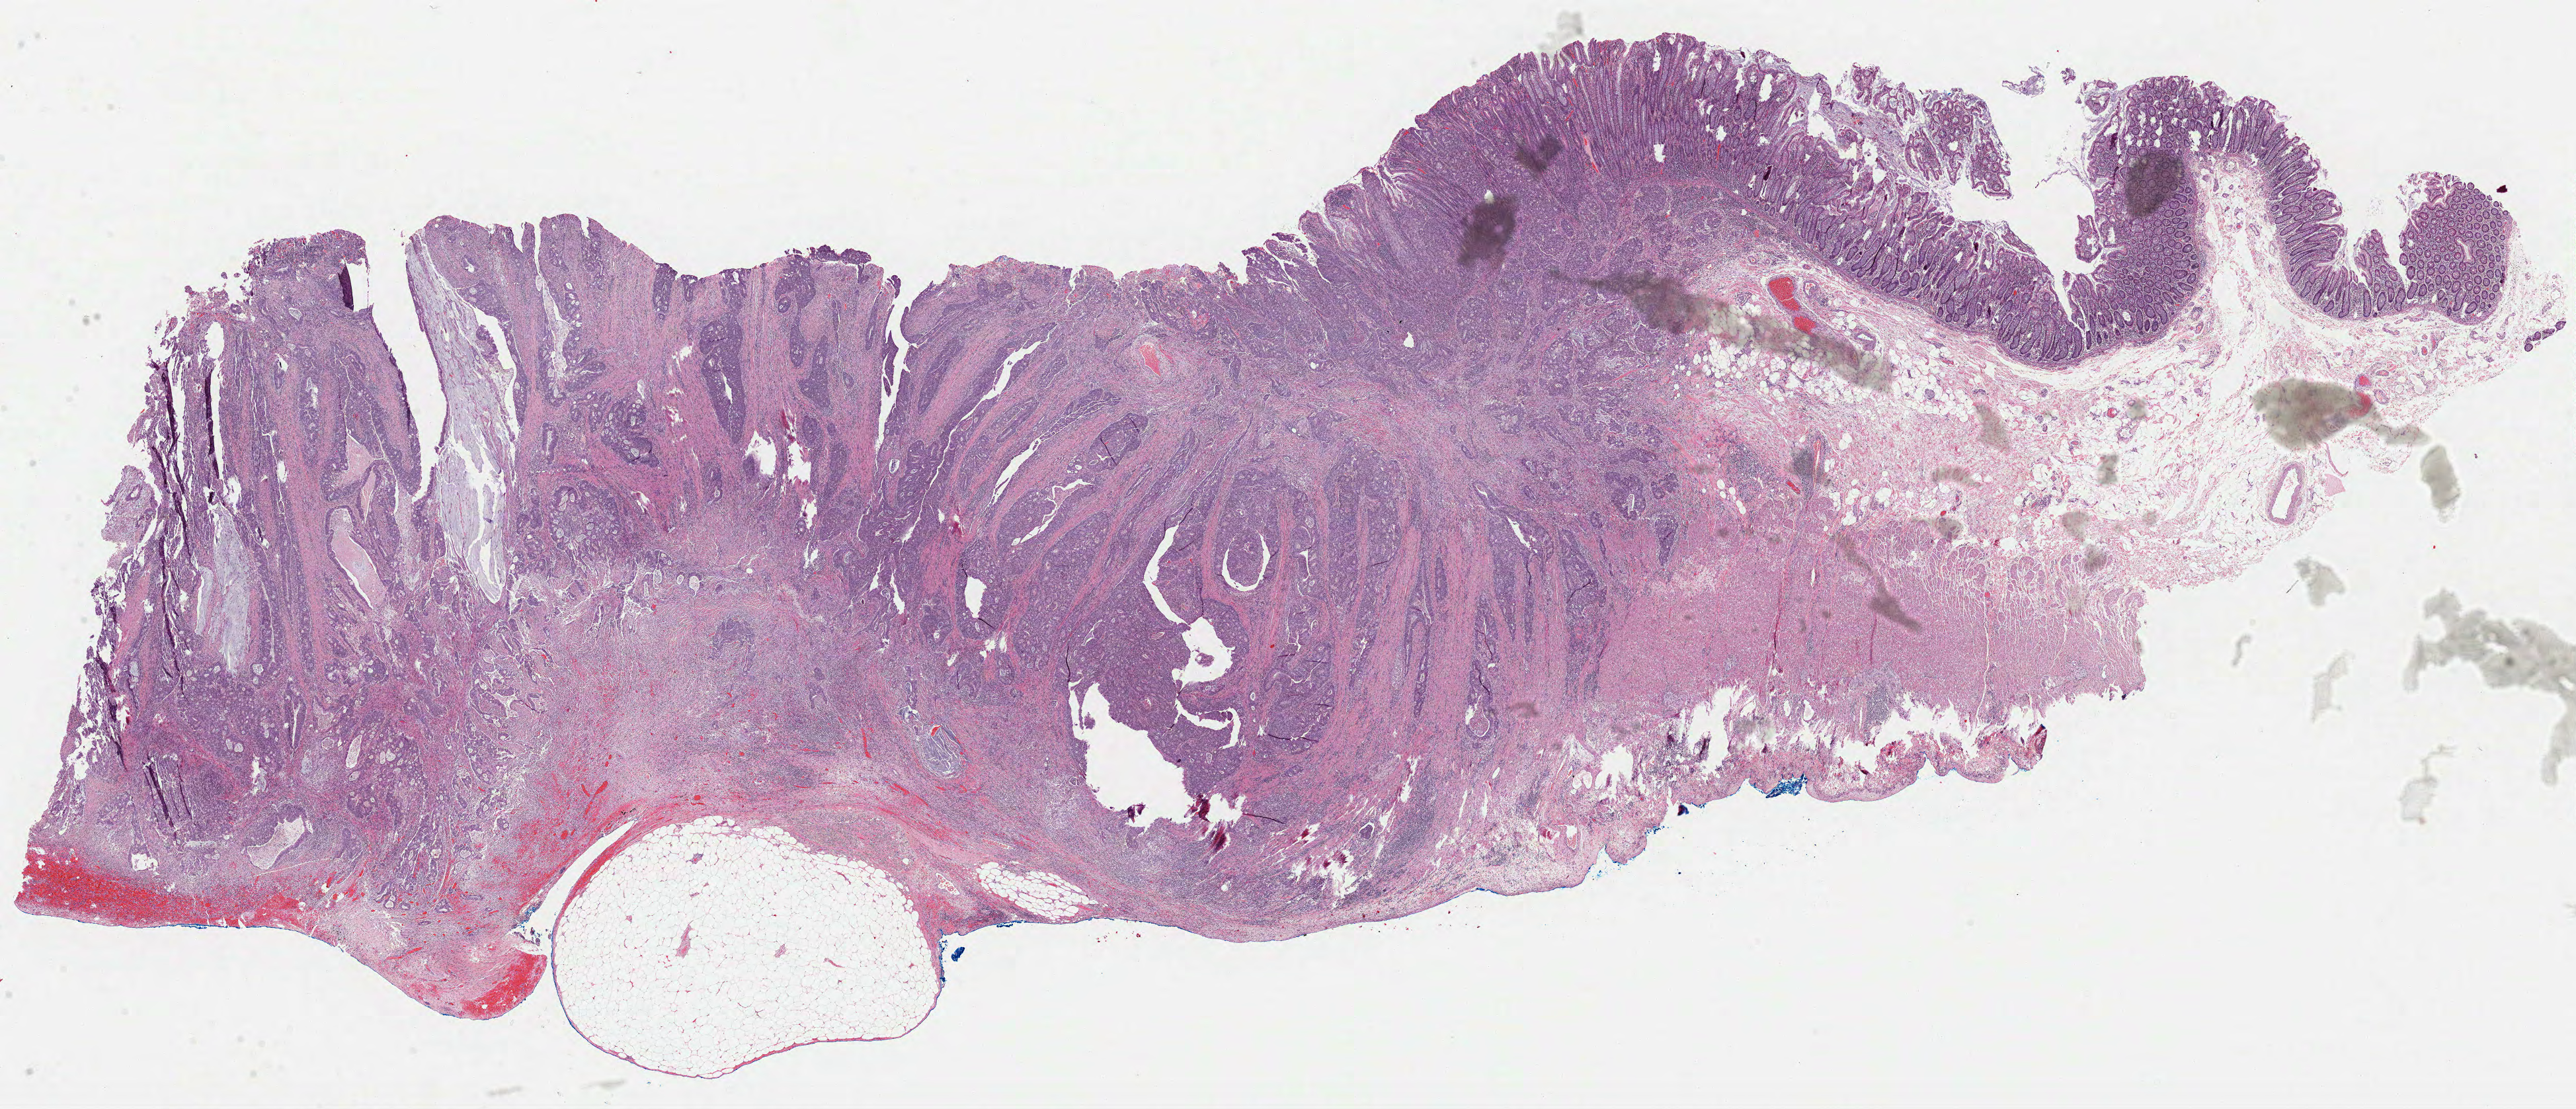
Digitized H&E-stained tissue section (whole slide), shown as a low-resolution overview of the whole scanned area (about 31.4 x 13.5 mm); formalin-fixed paraffin-embedded (FFPE) diagnostic section; sample: primary tumour, colon. Patient: male, age at initial diagnosis 62 years.
* pathologic diagnosis: Adenocarcinoma, NOS
* AJCC pathologic stage: IIIB (7th edition)